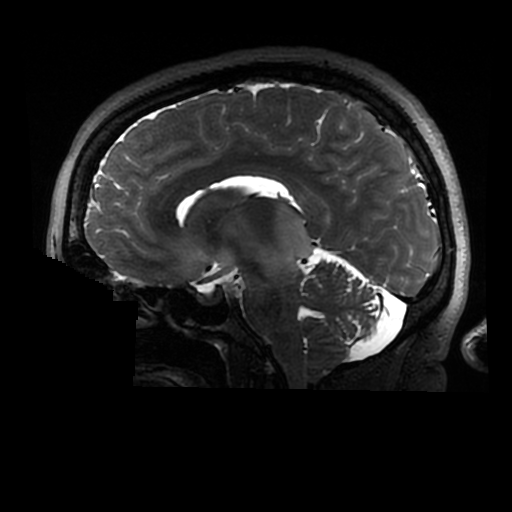
Brain MRI from a brain-tumour surgery series, one sagittal slice. Position 165 of 320 along the scan axis. 0.6 mm slice thickness. 512 × 512 image matrix. From the clinical record (not read from this slice): histopathology: Astrocytoma; WHO grade: 2; IDH mutation: yes.
Annotated regions visible in this slice (manually delineated by an expert):
- tumour: bounding box <270,203,314,269> (left, top, right, bottom; pixels)